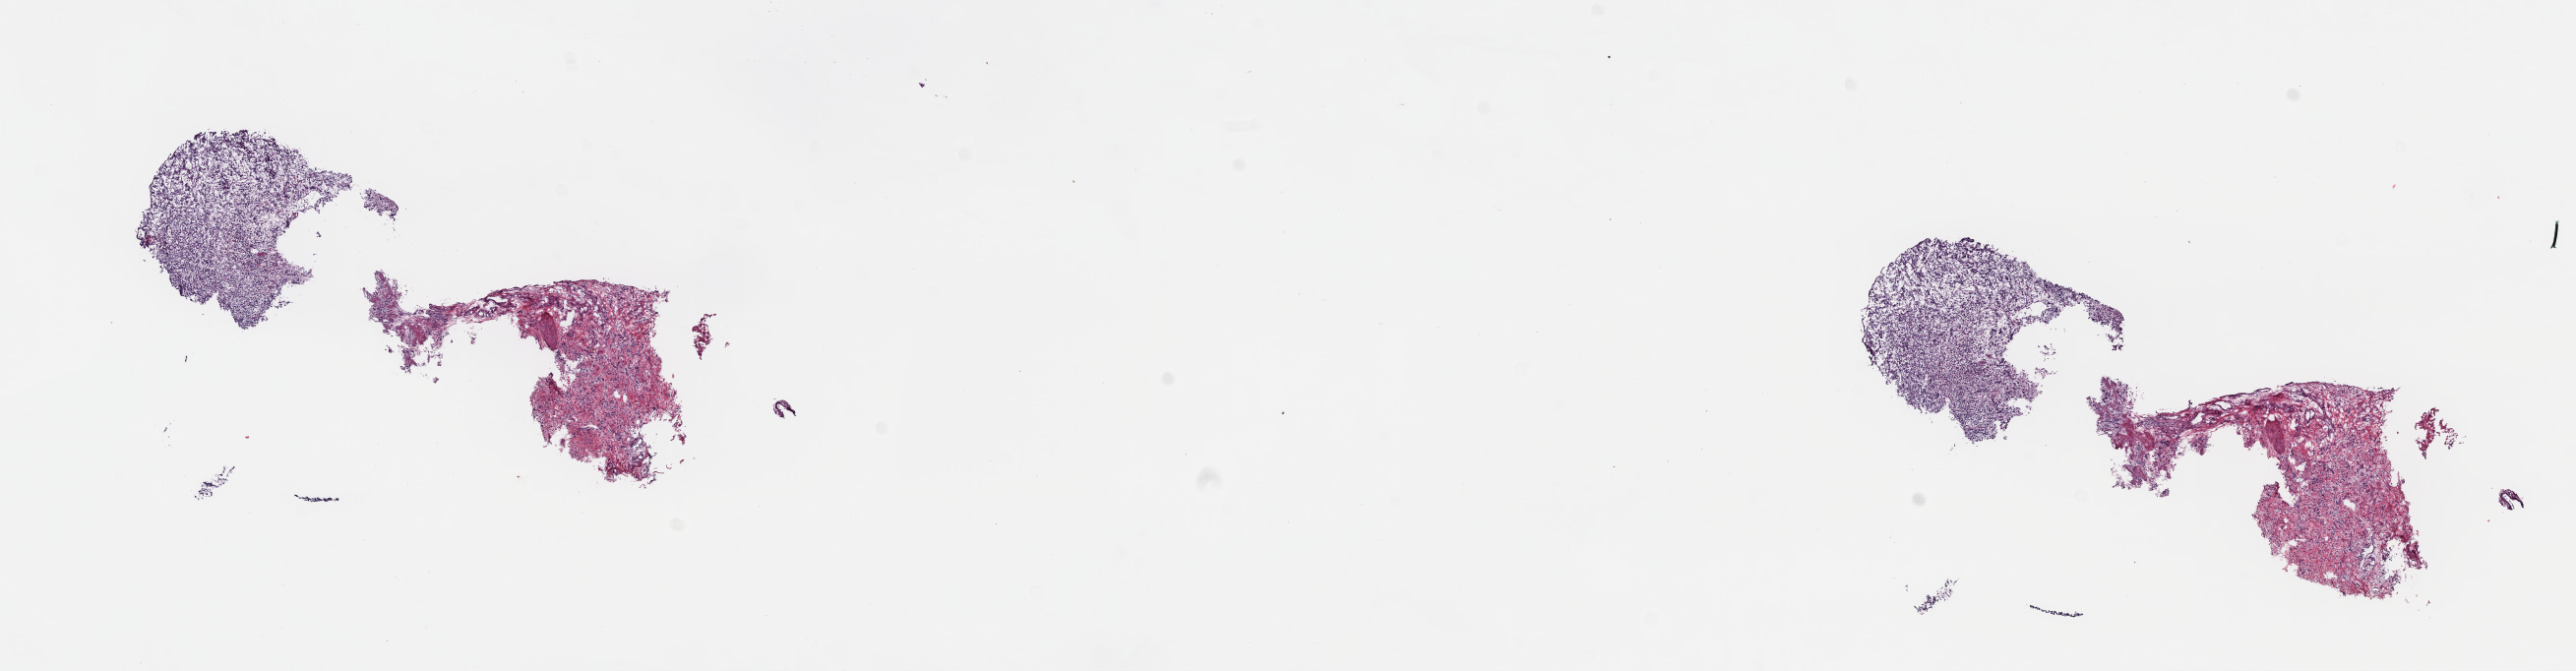
Digitized H&E tissue section (whole slide), low-resolution overview of the scanned area, about 20.6 x 5.4 mm (from a 40x scan), frozen section from the top of the tissue portion, stomach, primary tumour sample. Female patient; age at initial diagnosis 60 years.
Diagnosis: Mucinous adenocarcinoma.